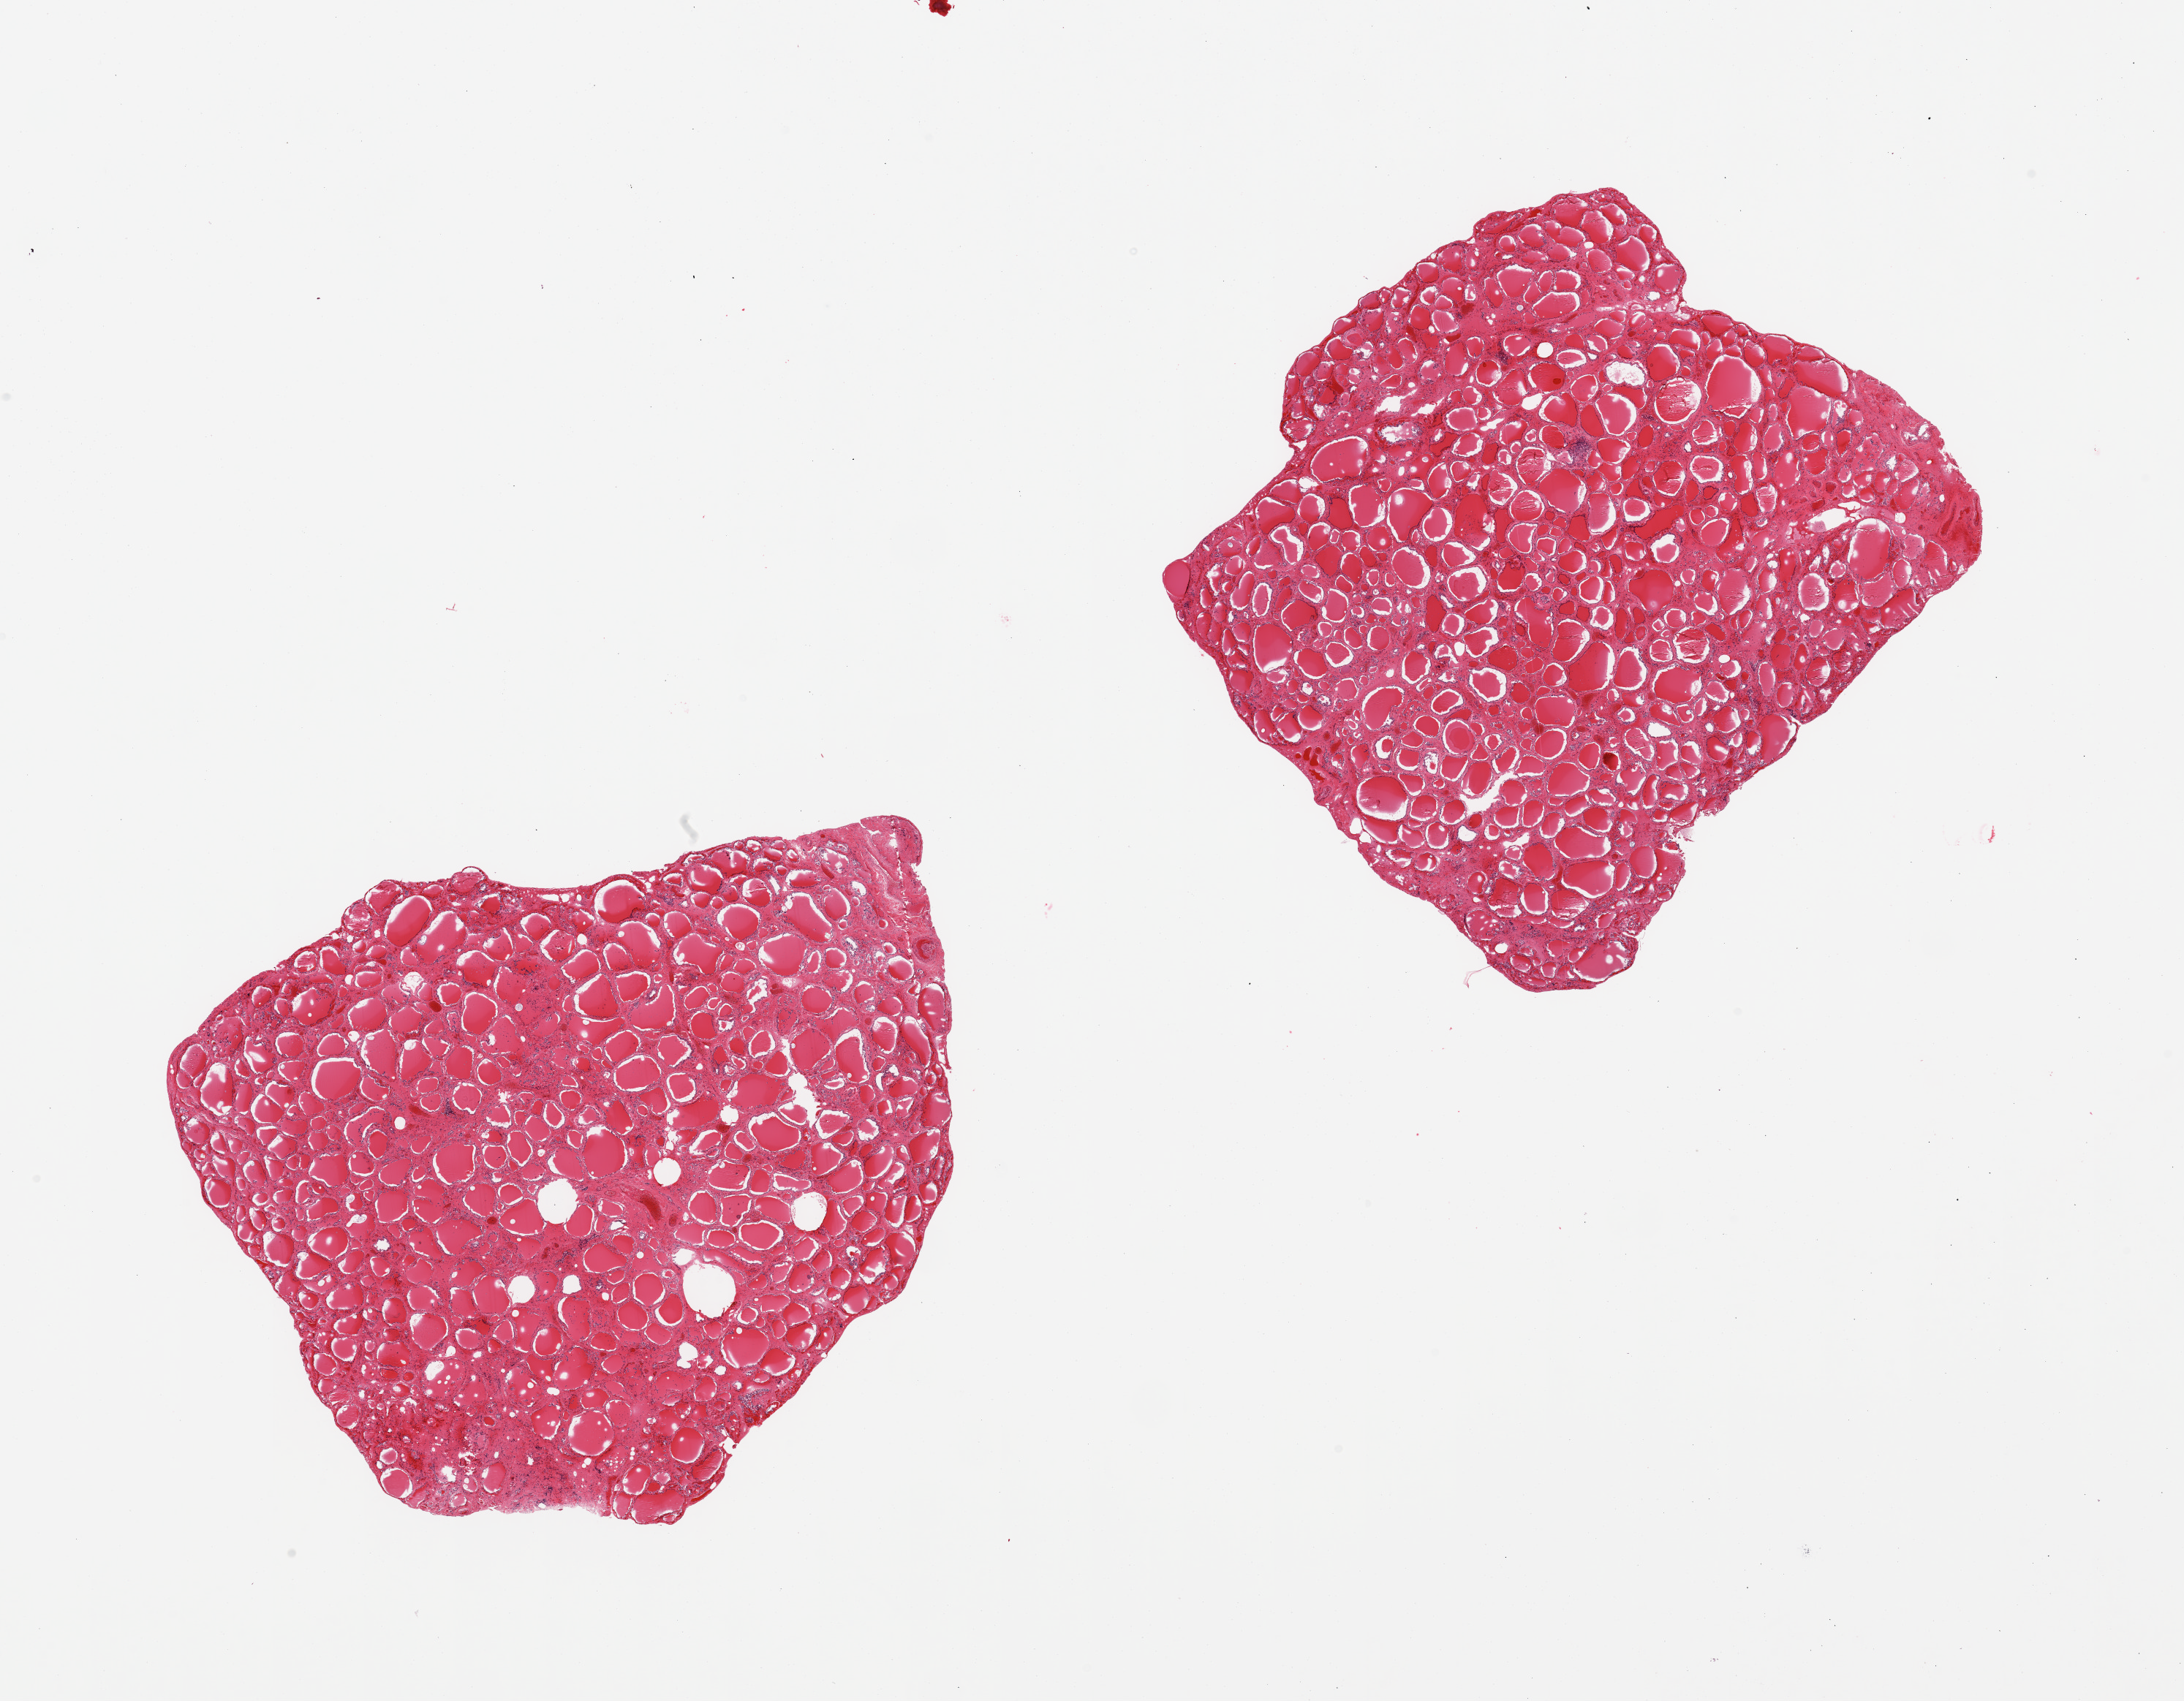
Digitized hematoxylin and eosin (H&E)-stained section — a low-resolution overview of the entire scanned area, about 23.6 x 18.4 mm (from a 20x scan). PAXgene-fixed, paraffin-embedded tissue. Sampled site (target tissue): thyroid. Donor tissue sample. Male donor.
Review note (as recorded): 2 pieces.